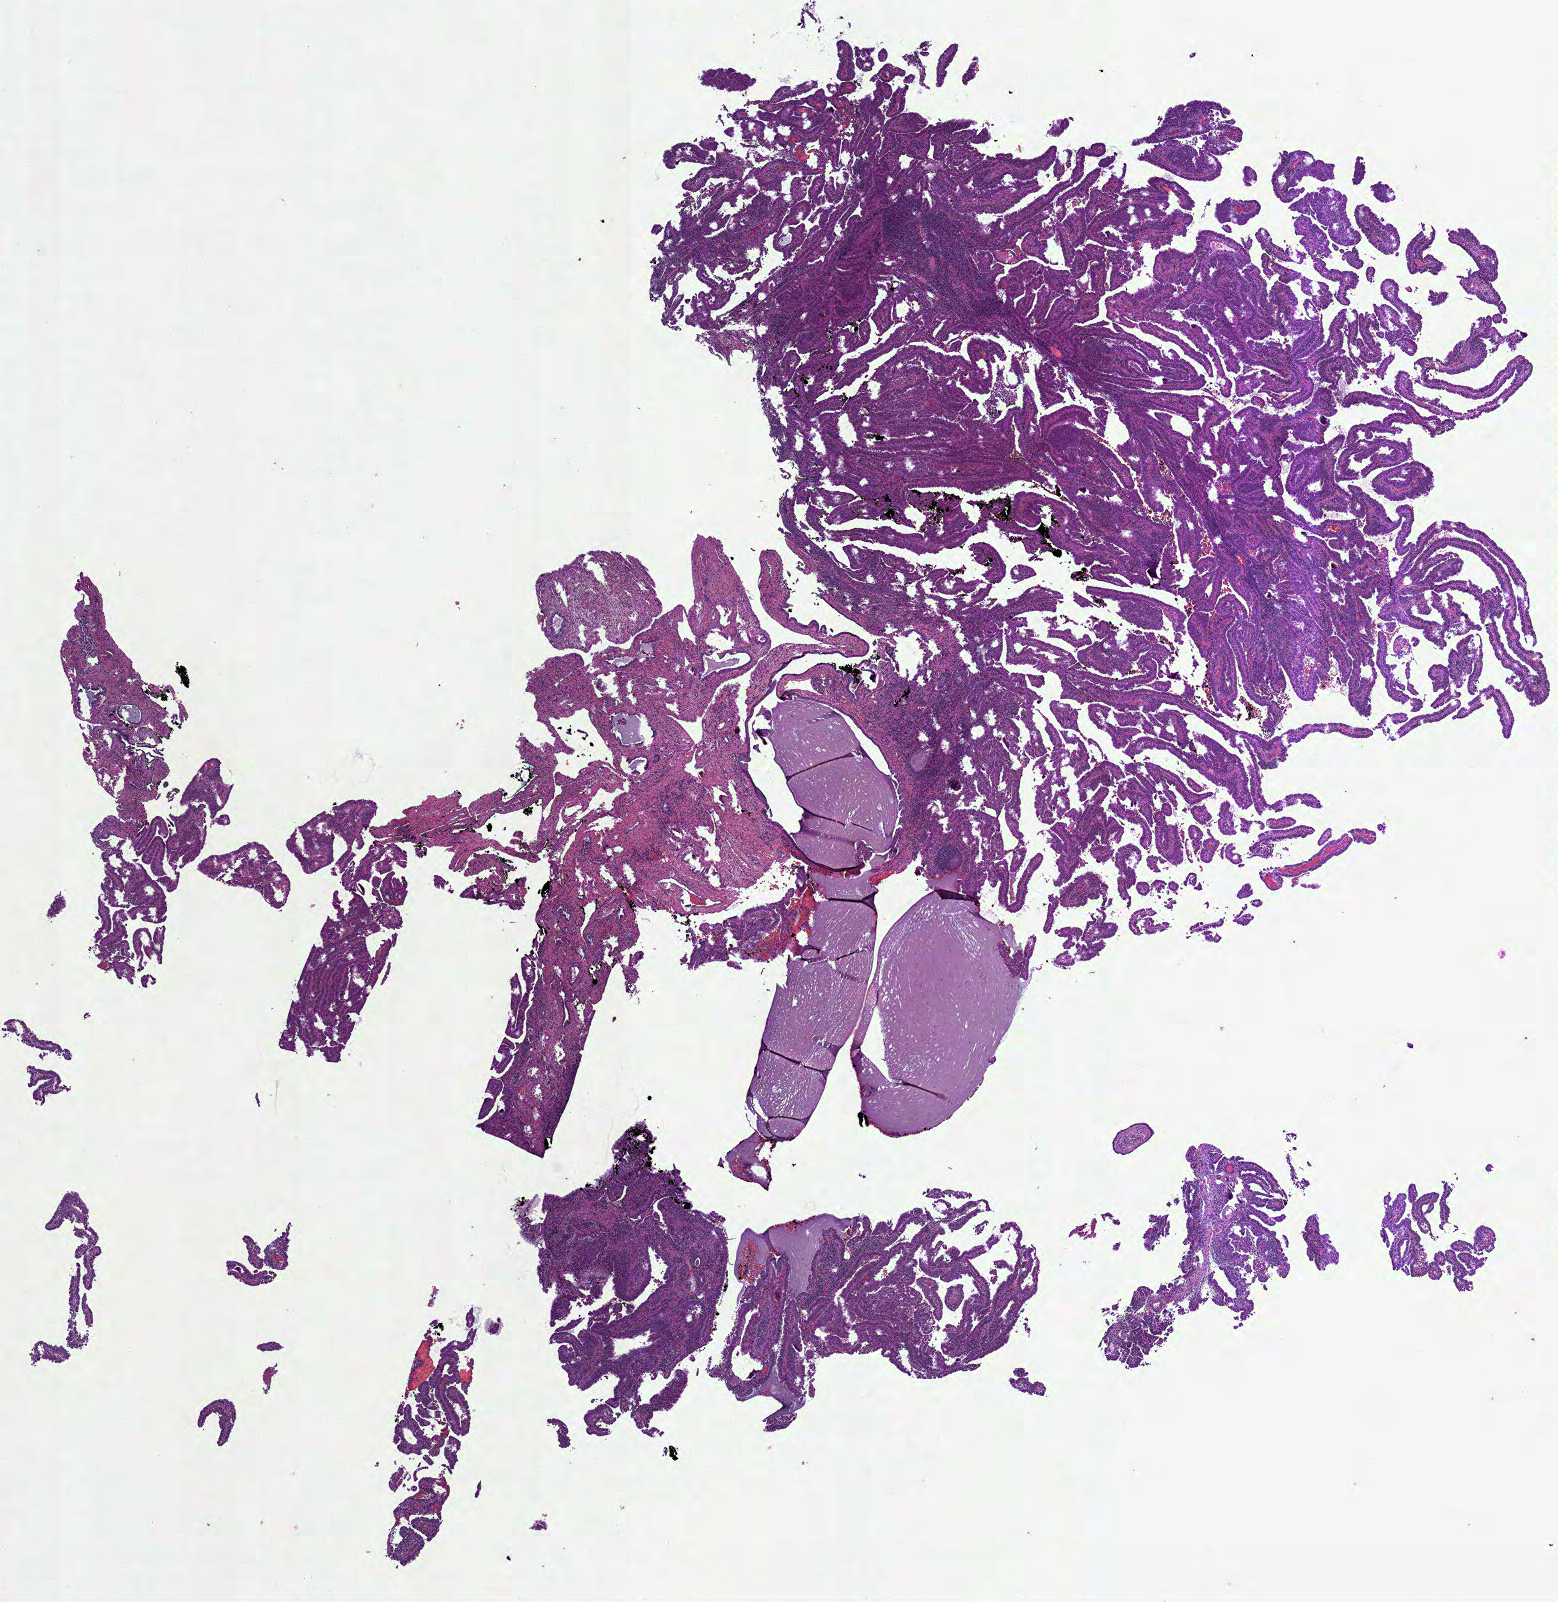
Whole-slide histology image, H&E, whole scanned area (about 12.6 x 12.9 mm) shown as a low-resolution overview; formalin-fixed paraffin-embedded (FFPE) diagnostic section; sample: primary tumour, uterus. Female patient; age at initial diagnosis 64 years. Histologic grade: G1 (well differentiated).
Histologic diagnosis: Endometrioid adenocarcinoma, NOS (endometrium). FIGO stage: II.